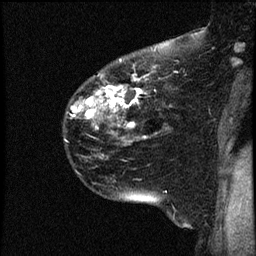
Breast MRI (dynamic contrast-enhanced), one sagittal slice. Position 36 of 44 along the scan axis. Dynamic contrast-enhanced study with each time point stored as its own series, time point 2 of 4 at this slice position (early post-contrast, ordered by acquisition time). 1.5 T. TE 4.2 ms, TR 17.7 ms. 2 mm slice thickness. 256 × 256 image matrix, field of view 200 × 200 mm. Female patient, age 52 years. Case-level facts recorded for this patient, not image findings: setting: breast cancer imaged before/during neoadjuvant chemotherapy; receptor status: HR-positive, HER2-negative.
Structures marked on this image (semi-automatically segmented with operator editing):
- analysis volume of interest (the breast-tissue region the enhancement analysis was run in; not a lesion): box from (x=63, y=48) to (x=163, y=147) px
- tumour enhancement mask (voxels above the 100 % enhancement threshold inside the analysis volume of interest): (x=71, y=79)–(x=146, y=128)